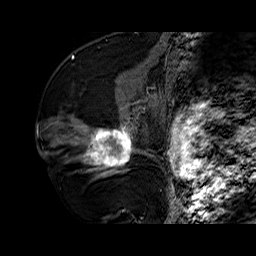
Breast MRI (dynamic contrast-enhanced), one sagittal slice; slice 33 of 60 in the series (ordered by position); dynamic contrast-enhanced series, time point 2 of 6 at this slice position (early post-contrast); 1.5 T; TE 6.4 ms, TR 32.7 ms; 4 mm slice thickness; 256 × 256 image matrix. Female patient. From the clinical record (not read from this slice): setting: breast cancer imaged before/during neoadjuvant chemotherapy; receptor status: HR-positive, HER2-negative.
Annotated regions visible in this slice (semi-automatic segmentation, software-assisted and operator-edited):
- analysis volume of interest (the breast-tissue region the enhancement analysis was run in; not a lesion): bounding box [x1, y1, x2, y2] px = [73, 110, 141, 178]
- tumour enhancement mask (voxels above the 100 % enhancement threshold inside the analysis volume of interest): [83, 126, 133, 172]